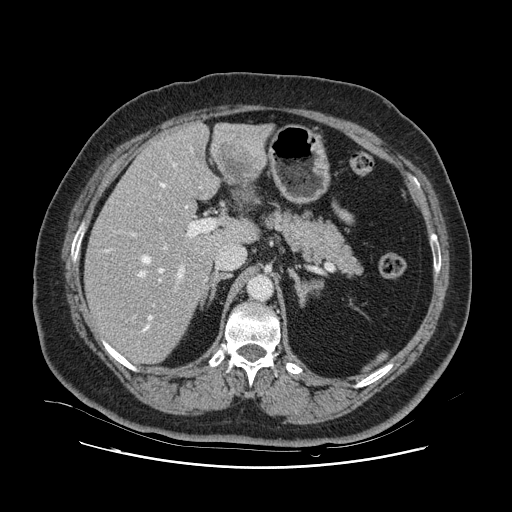
Contrast-enhanced abdominal CT, one axial slice; intravenous contrast given; soft-tissue window (W 400 / L 40 HU); 2.5 mm slice thickness; 512 × 512 image matrix, field of view 391 × 391 mm. Female patient, age 73 years. Case-level facts recorded for this patient, not image findings: diagnosis: colorectal cancer liver metastases, imaged before liver resection; multiple liver metastases: no; largest metastasis: 7 cm; disease in both lobes: no.
Structures marked on this image (manually delineated by an expert):
- hepatic veins: bounding box [x1, y1, x2, y2] px = [105, 163, 202, 332]
- liver: [86, 122, 268, 363]
- planned liver remnant (the part of the liver to remain after resection): [86, 151, 241, 363]
- portal vein (with intrahepatic branches): [132, 219, 215, 306]
- liver metastasis: [219, 144, 257, 176]